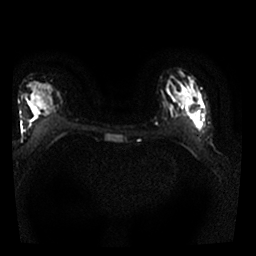
Breast MRI, one axial slice. Diffusion-weighted series; image 2 of 4 stored at this slice position (different b-values; order by instance number). 1.5 T. 256 × 256 image matrix, field of view 300 × 300 mm. Female patient.
Annotated regions visible in this slice (outlined manually by an expert reader):
- tumour on diffusion-weighted imaging: bounding box <189,110,202,129> (left, top, right, bottom; pixels)